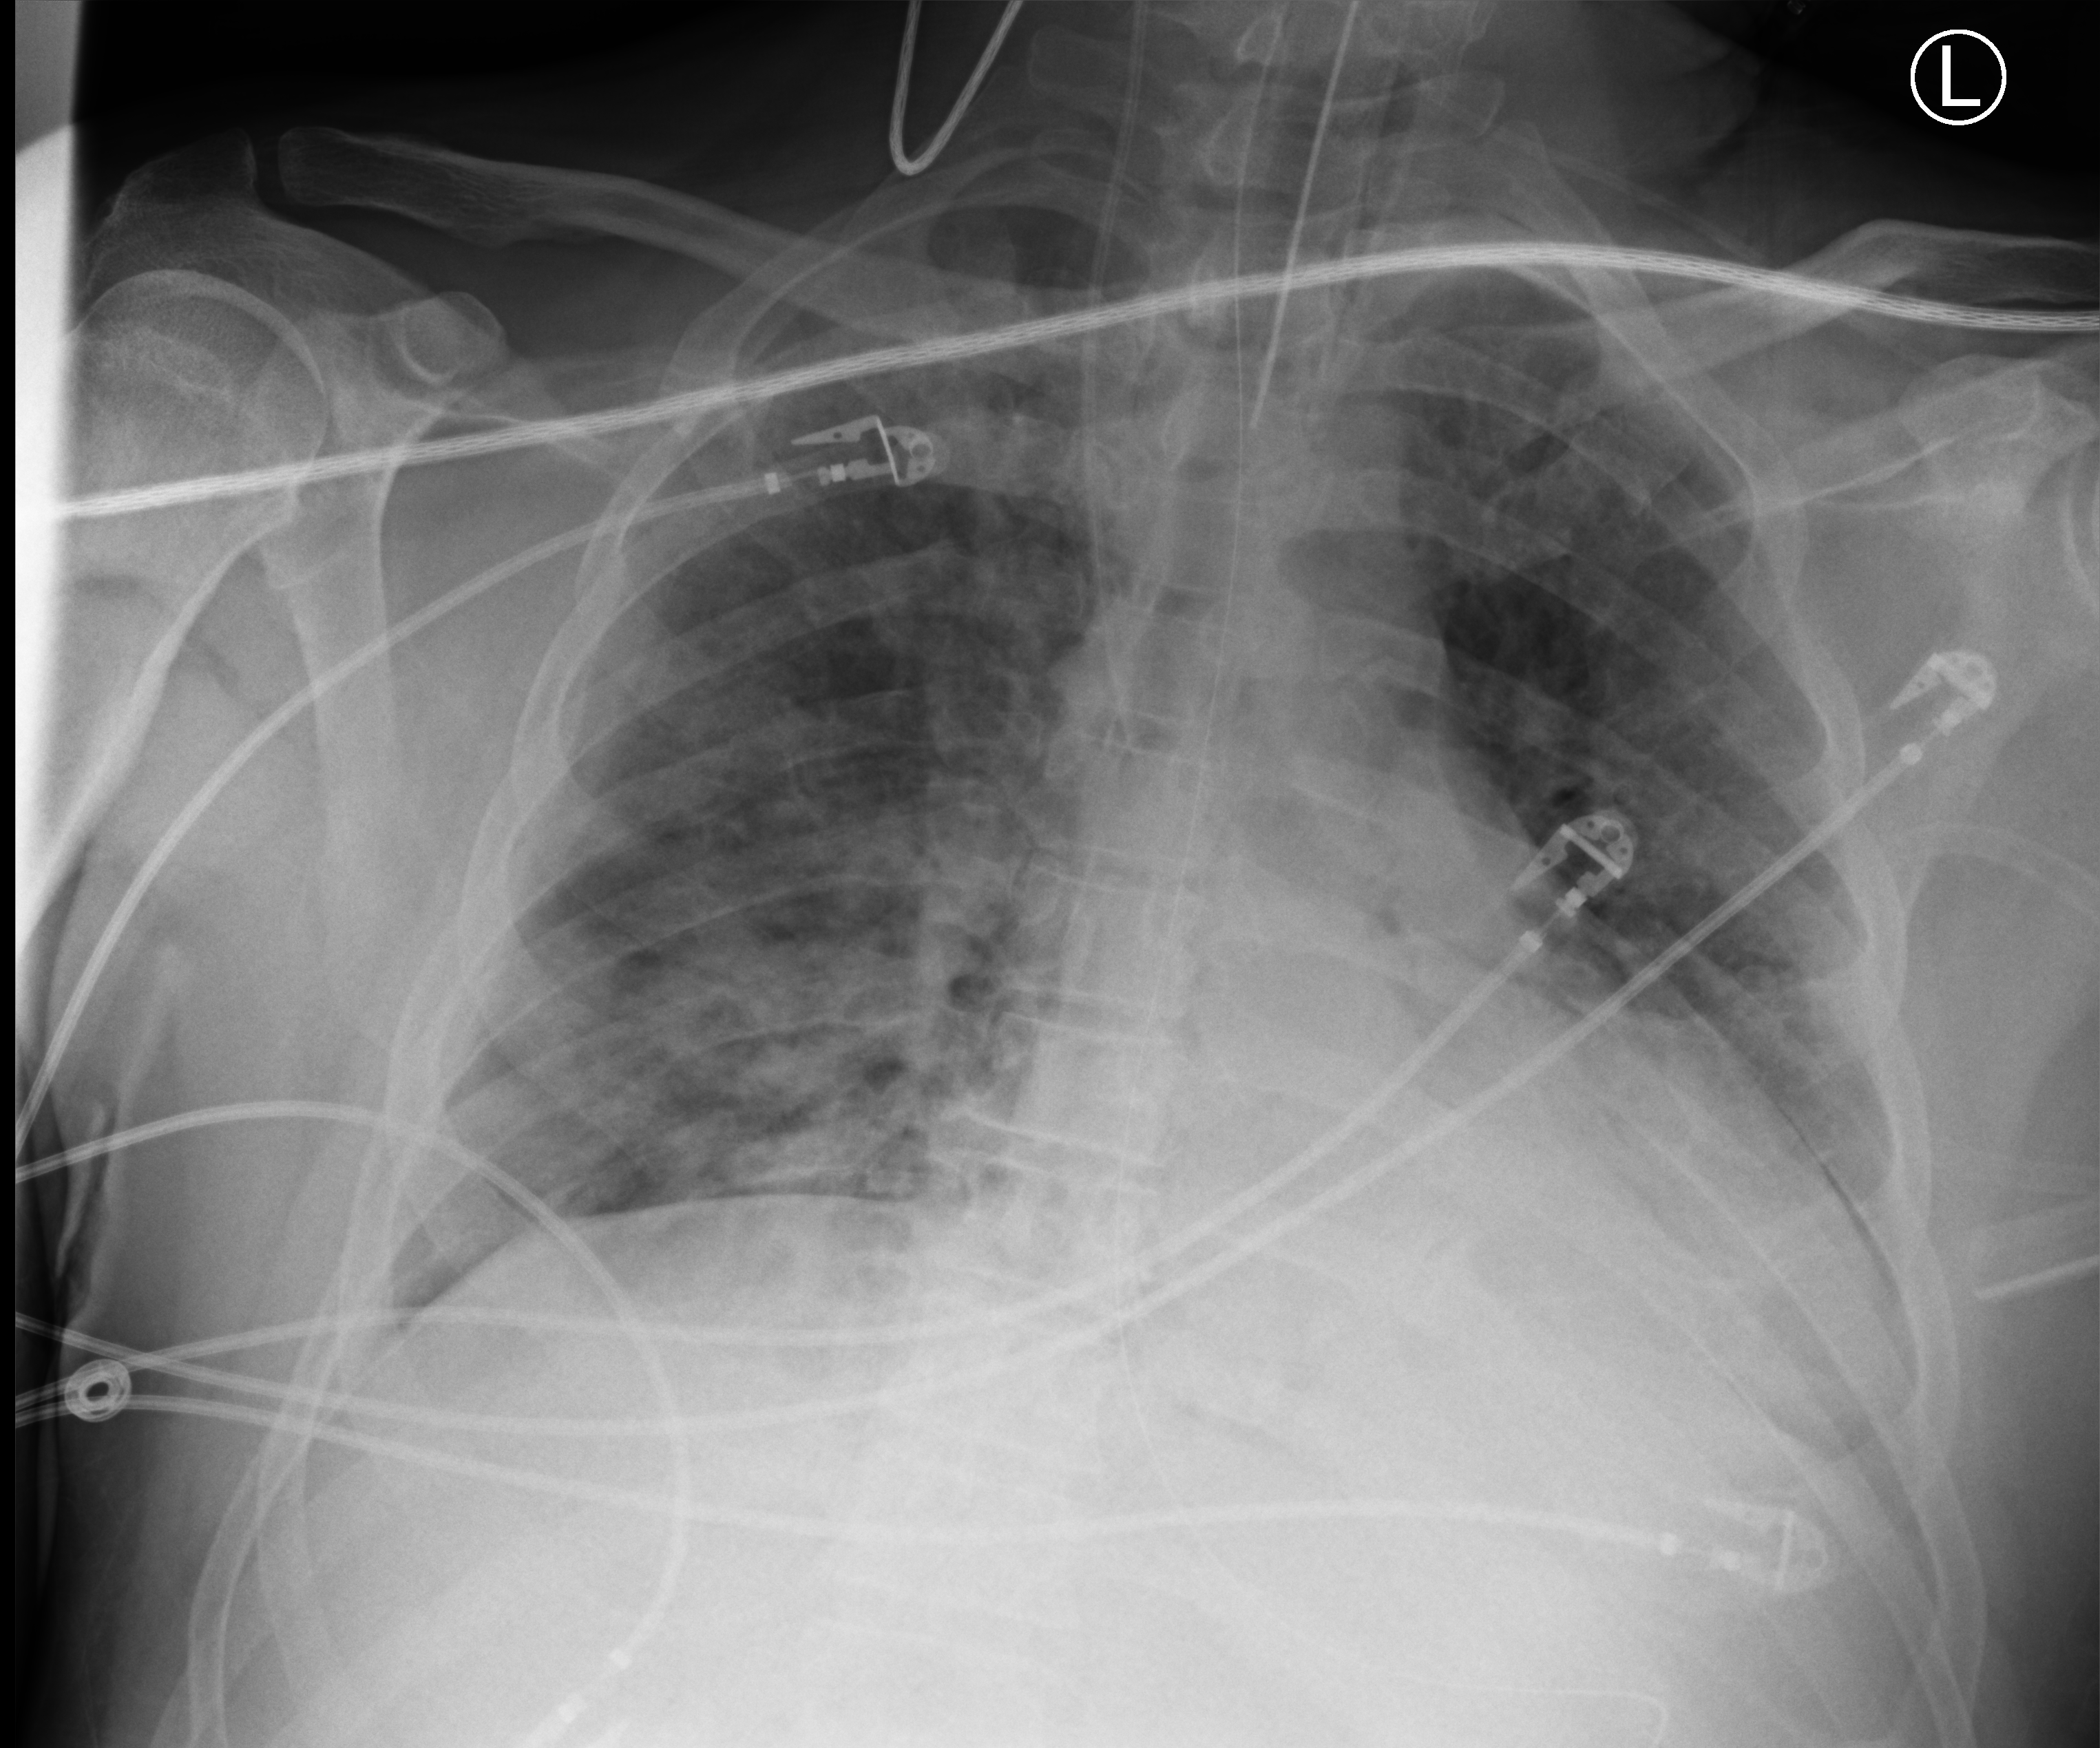
Bedside chest radiograph (computed radiography), anteroposterior (AP) projection. Patient hospitalised with COVID-19; male, aged 18–59 years.
Admission-level facts for this patient (not findings on this image; timing relative to this image not recorded):
- mechanically ventilated during this hospital stay: yes
- admitted to intensive care during this hospital stay: no